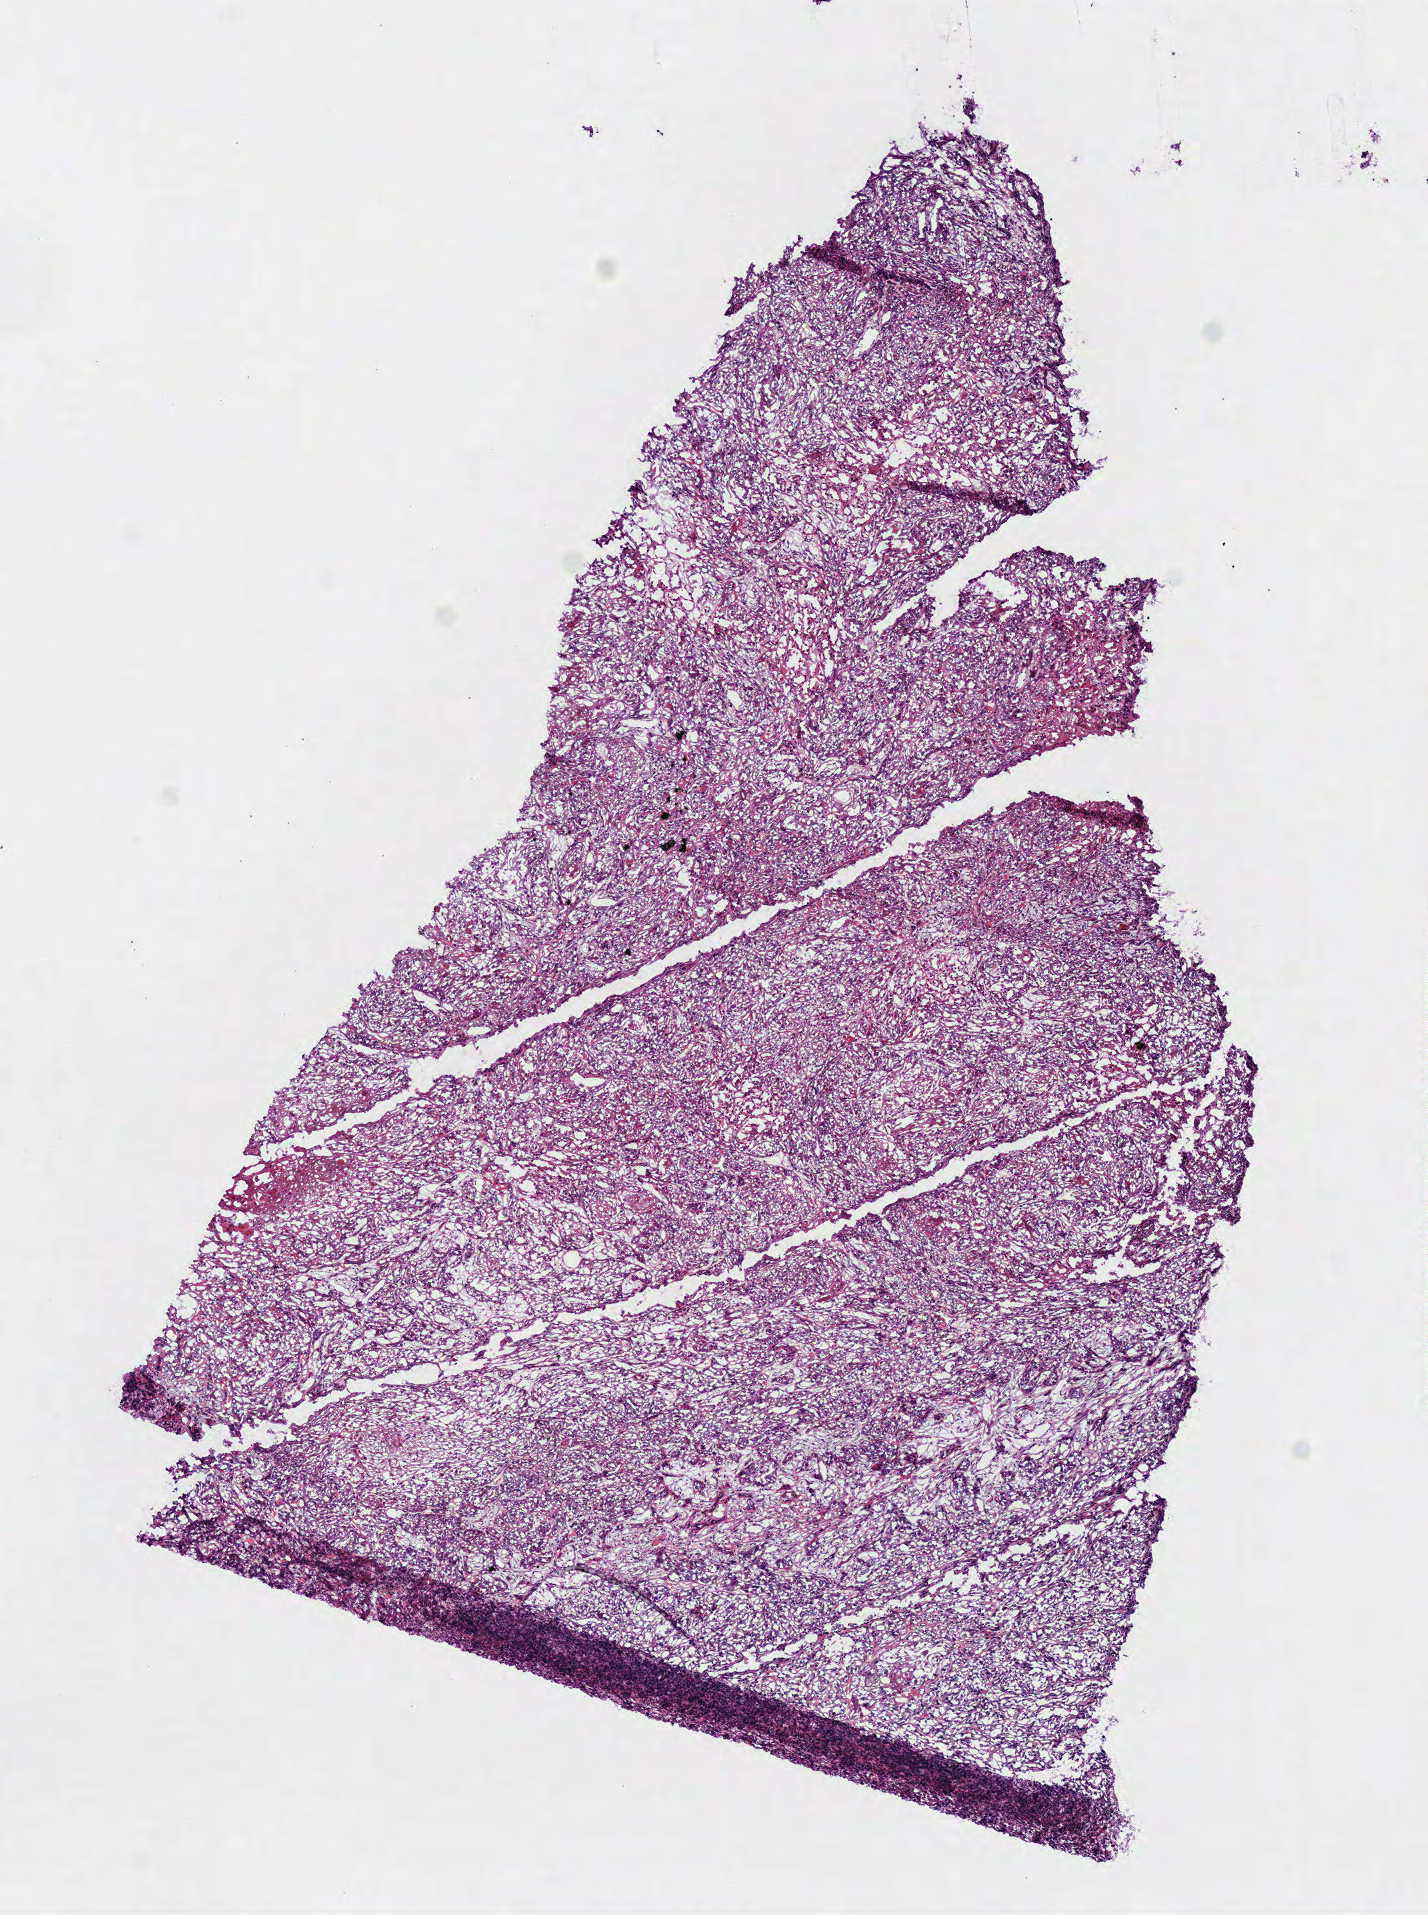
H&E whole-slide image, a low-resolution overview of the entire scanned area, about 5.6 x 7.5 mm; frozen section from the bottom of the tissue portion; primary tumour sample from the head and neck. Patient: male, age at initial diagnosis 26 years. Histologic grade: G2 (moderately differentiated). Pathologist review of this section (percent, as recorded): tumour cells 95%, tumour nuclei 85%, normal cells 0%, stromal cells 5%, necrosis 0%.
AJCC pathologic stage: IVA (7th edition). Pathologic diagnosis: Squamous cell carcinoma, NOS (tongue, NOS). Lymph nodes positive (case pathology): 2 of 55 examined.